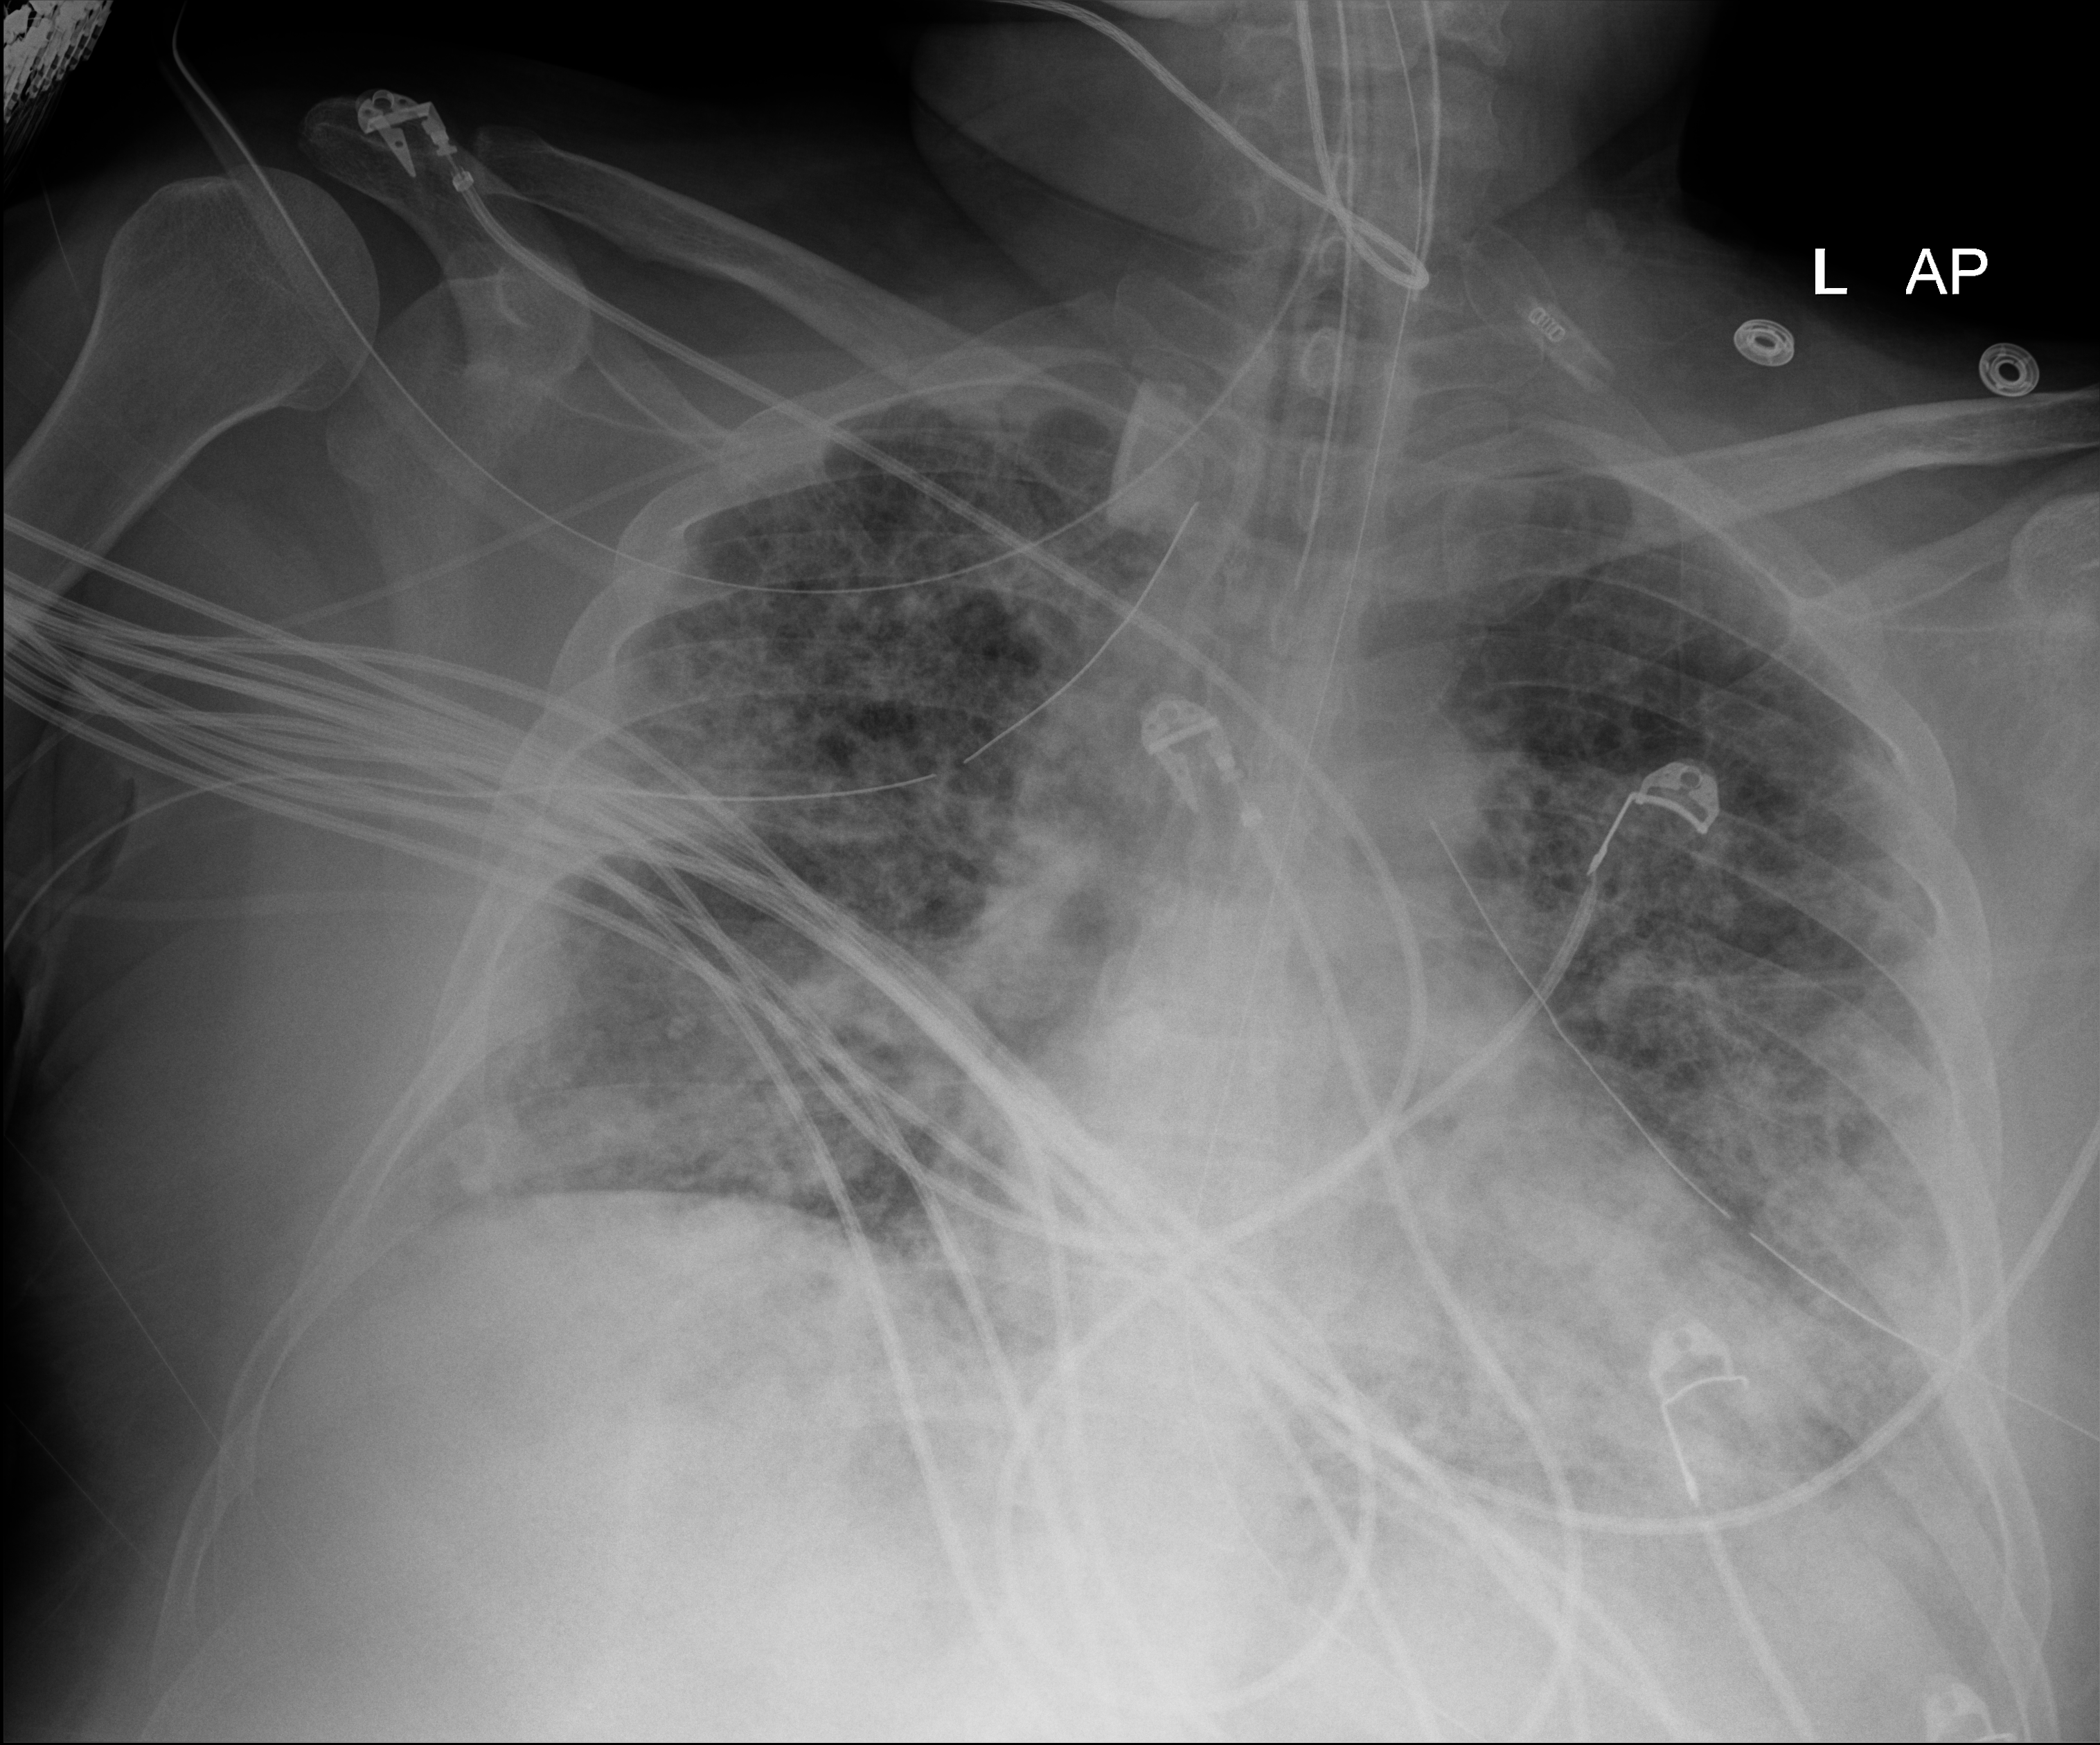
Chest X-ray (portable). Male patient hospitalised with COVID-19, age 18–59 years.
Hospital-stay facts (about this admission, not read from this image; timing relative to this image not recorded): chronic kidney disease (admission record): no.